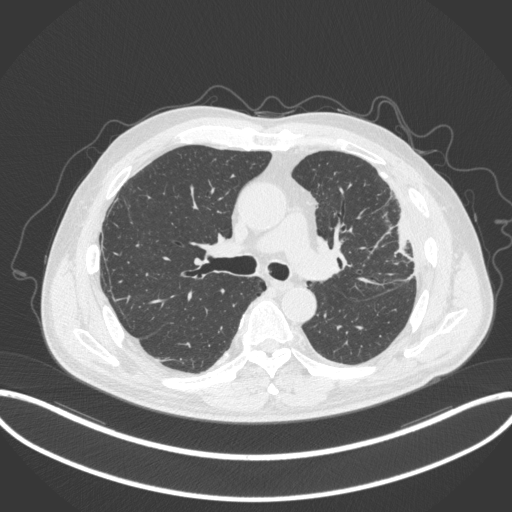
Chest CT, one axial slice; slice 213 of 382 in the series (ordered by position); reconstruction kernel B31f; 120 kVp; lung window (W 1500 / L -600 HU); 512 × 512 image matrix. Patient: male, 64 years. From the clinical record (not read from this slice): clinical TNM (as recorded): T4 N1 M0.
Outlined on this slice (bounding box drawn by a radiologist):
- lung tumour (recorded histology: adenocarcinoma): bounding box <389,211,418,263> (left, top, right, bottom; pixels)